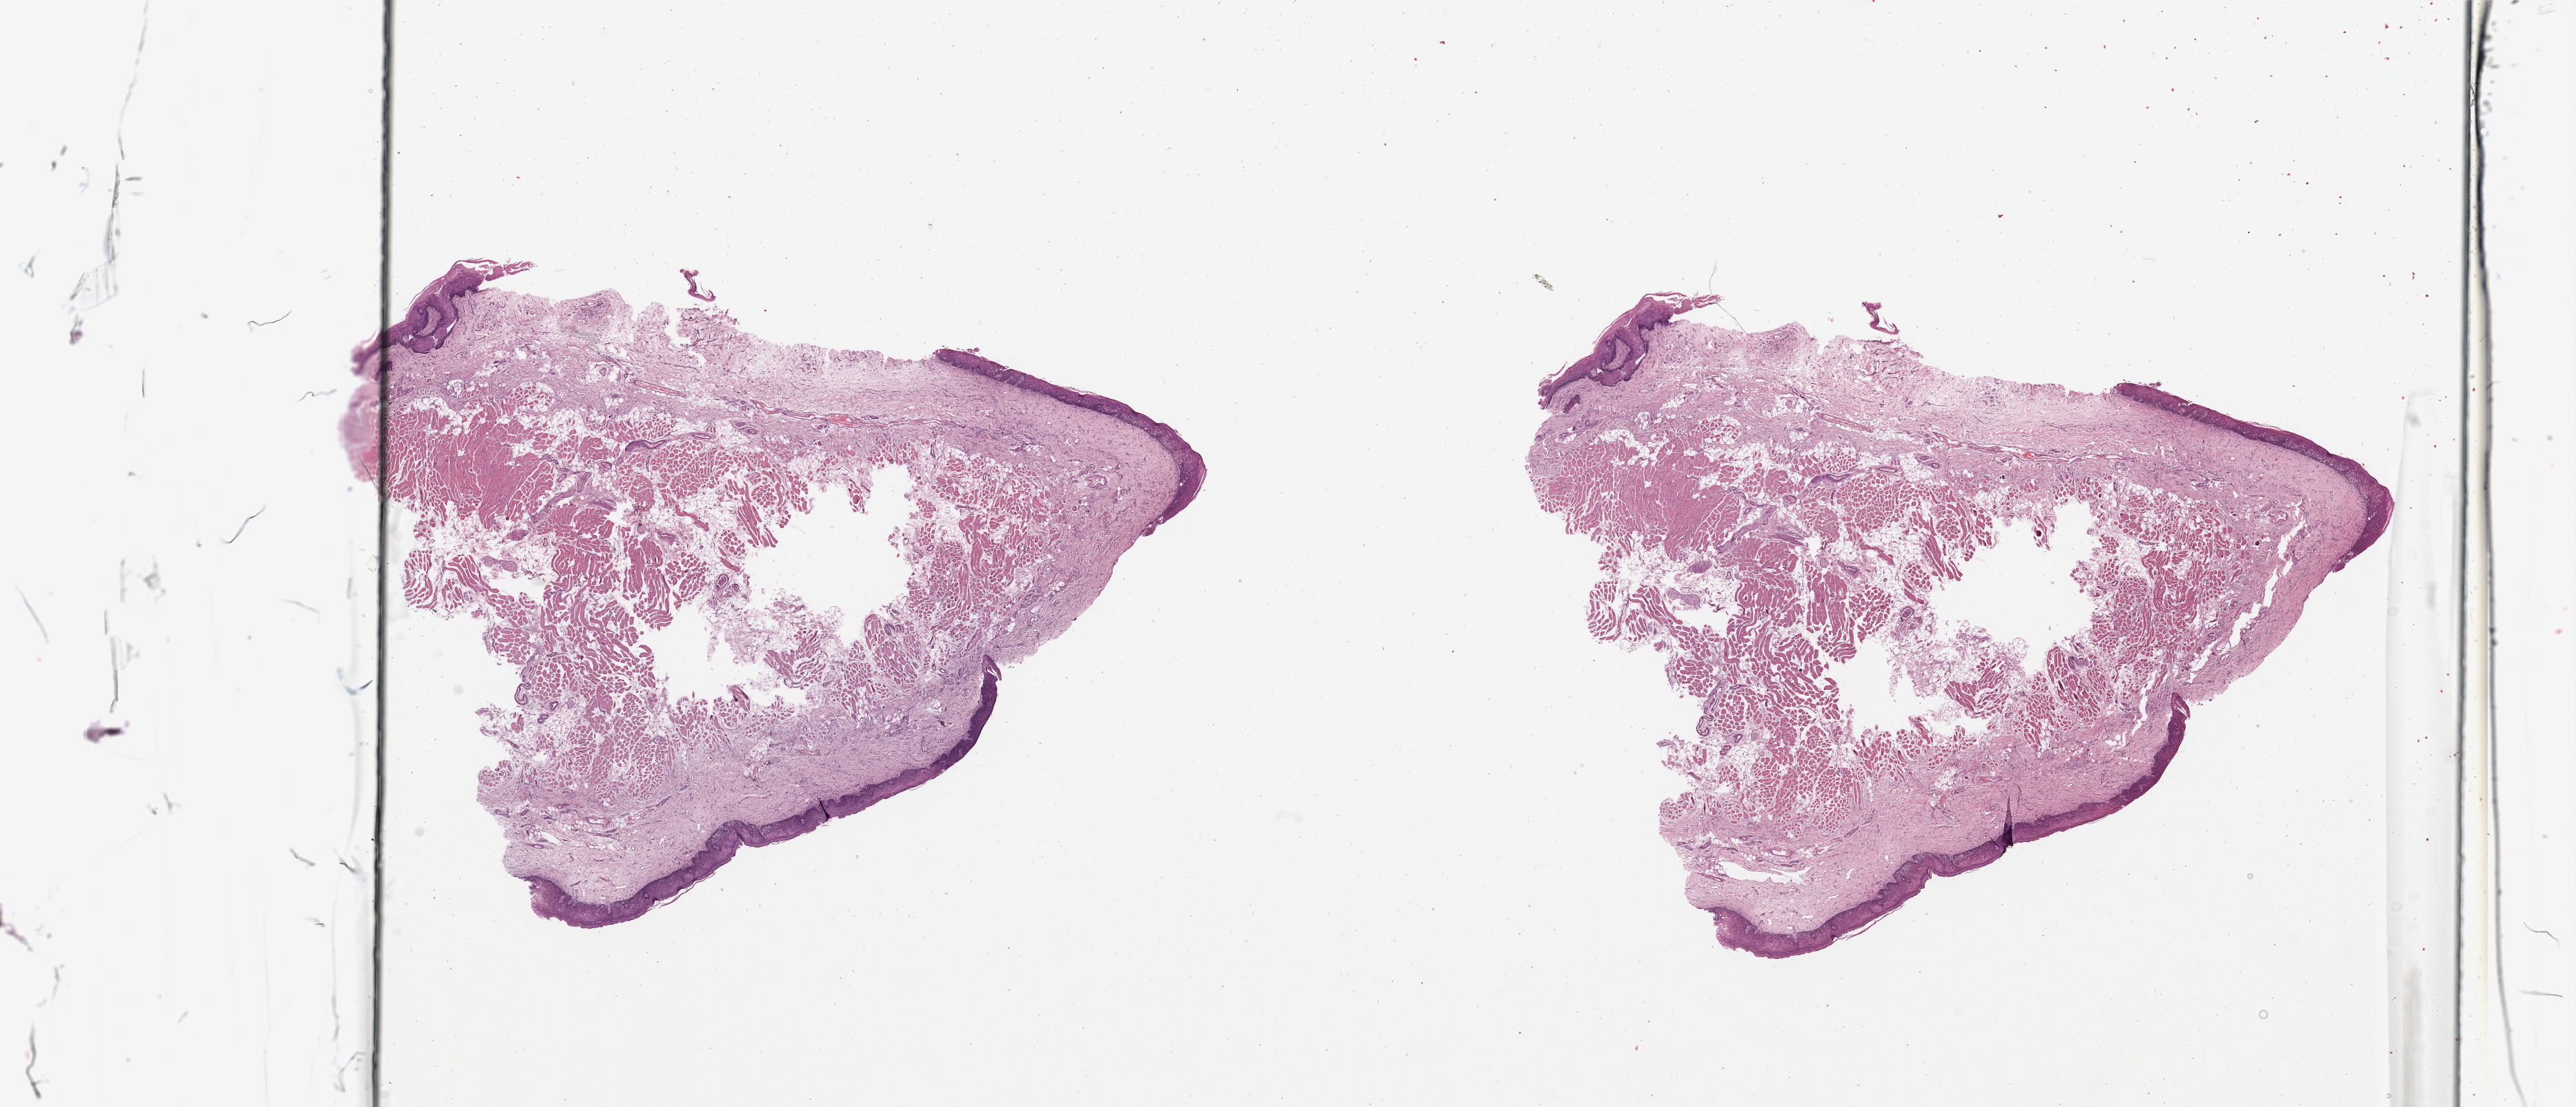
Hematoxylin and eosin (H&E) stained whole-slide image — low-resolution overview of the scanned area, about 29.5 x 12.7 mm. Normal (non-tumour) tissue sample, sampled site: tongue. 60-year-old female patient.
• this section: normal (non-tumour) tissue from the same patient
• patient diagnosis: Squamous cell carcinoma, NOS (tongue, NOS)